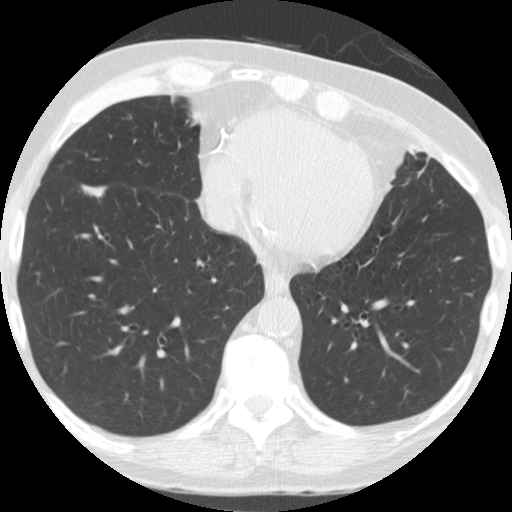
Low-dose screening chest CT, one axial slice; slice 71 of 182 in the series (ordered by position); reconstruction kernel STANDARD; 120 kVp; lung window (W 1500 / L -600 HU); 2.5 mm slice thickness; 512 × 512 image matrix.
Outlined on this slice (expert manual segmentation):
- lesion 1 (tumor, lower lobe of right lung): bounding box <82,185,106,198> (left, top, right, bottom; pixels)